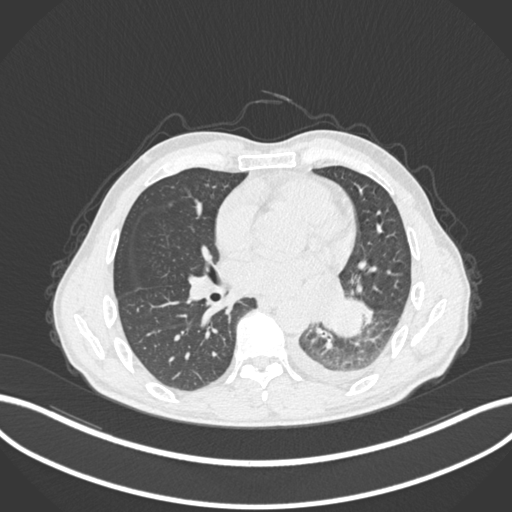
Chest CT, one axial slice. Position 113 of 222 along the scan axis. Reconstruction kernel B30f. 120 kVp. Lung window (W 1500 / L -600 HU). 1 mm slice thickness. 512 × 512 image matrix. Male patient, age 47 years. Case-level facts recorded for this patient, not image findings: clinical TNM (as recorded): T3 N1 M1c; histopathological grade: G3.
Annotated regions visible in this slice (bounding box drawn by a radiologist):
- lung tumour (recorded histology: small cell carcinoma): bounding box (x1, y1, x2, y2) in pixels: (321, 293, 365, 340)